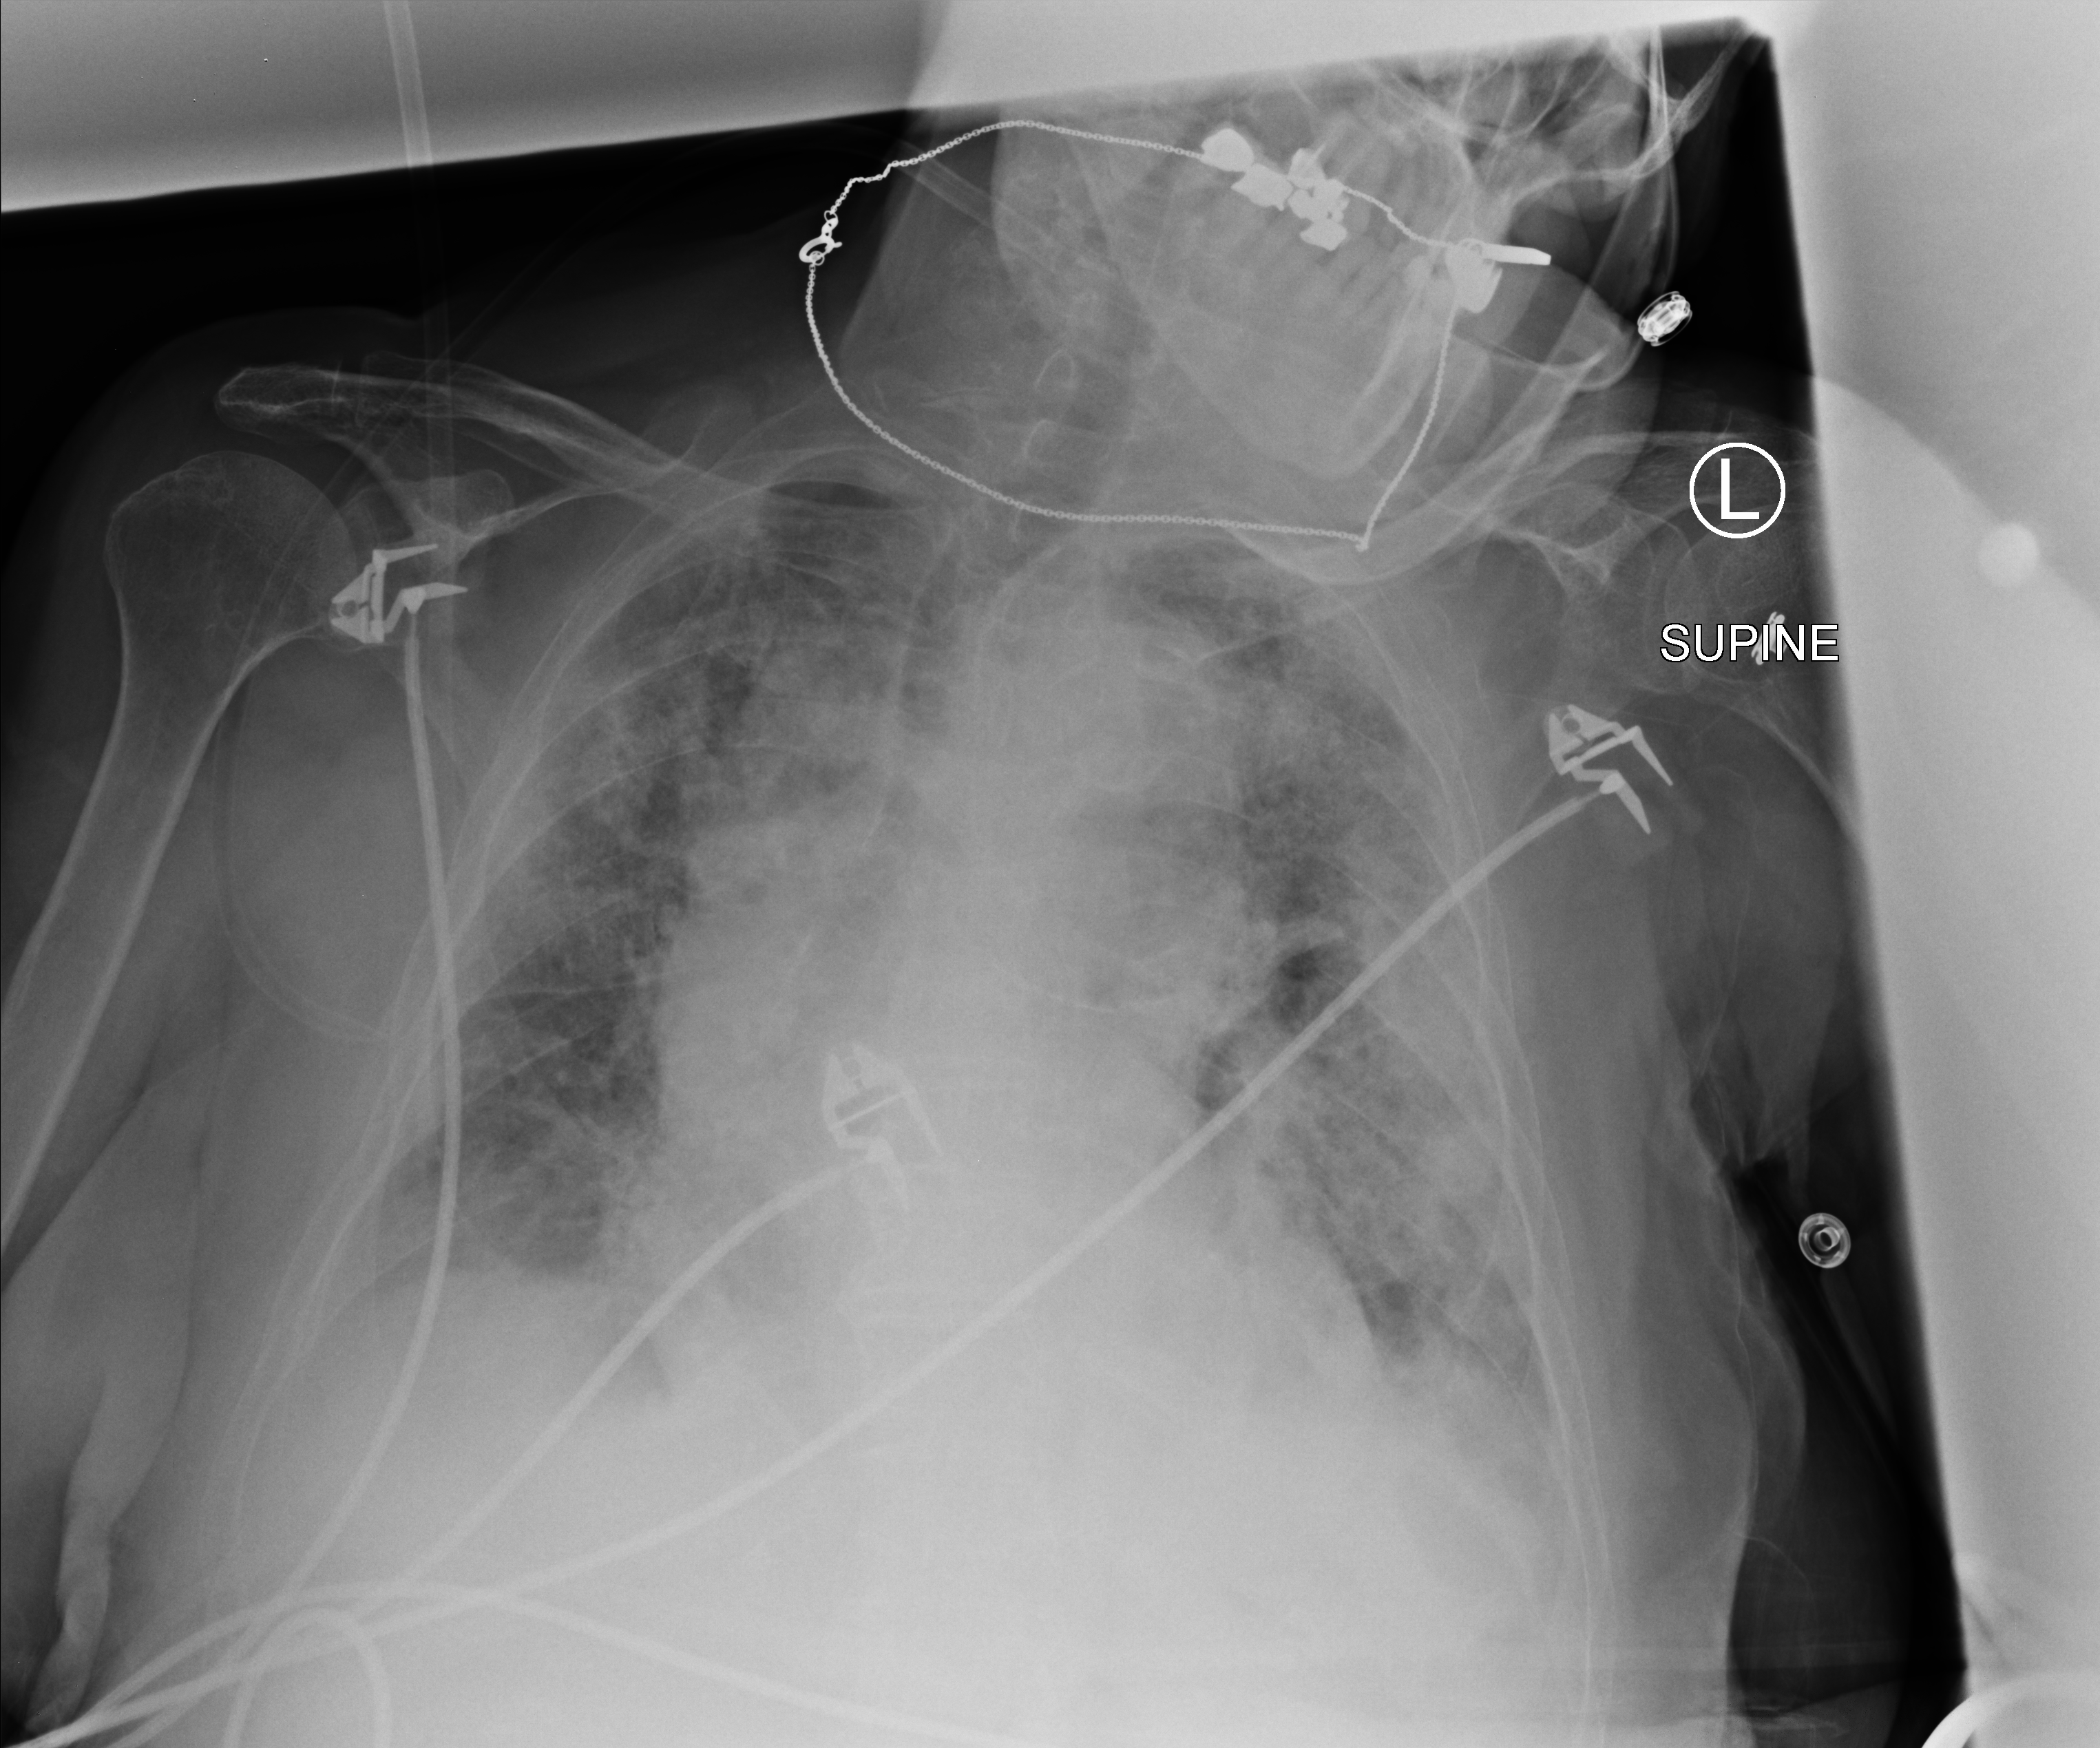
Bedside chest radiograph (computed radiography). Patient hospitalised with COVID-19; female, aged 75–90 years.
From the hospital-stay record, not from the radiograph (when in the stay this image was taken is not recorded): admitted to intensive care during this hospital stay: no.